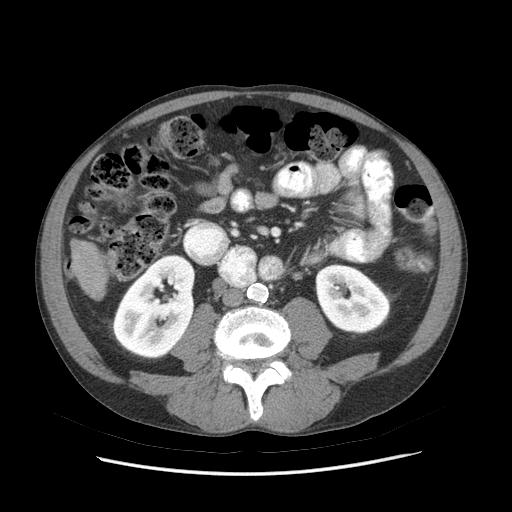
Contrast-enhanced abdominal CT (liver protocol), one axial slice; position 11 of 89 along the scan axis; 140 kVp; soft-tissue window (W 400 / L 40 HU); 2.5 mm slice thickness; 512 × 512 image matrix, field of view 380 × 380 mm. From the clinical record (not read from this slice): diagnosis: hepatocellular carcinoma (patient treated with transarterial chemoembolisation; whether this scan precedes or follows treatment is not stated here); TNM stage (as recorded): Stage-IIIB; Child-Pugh class: A; tumour differentiation: moderately differentiated.
Structures marked on this image (semi-automatically segmented with operator editing):
- liver parenchyma outside the tumour (the mass and vessels are separate outlines, so this box may not span the whole liver): box from (x=70, y=240) to (x=106, y=298) px